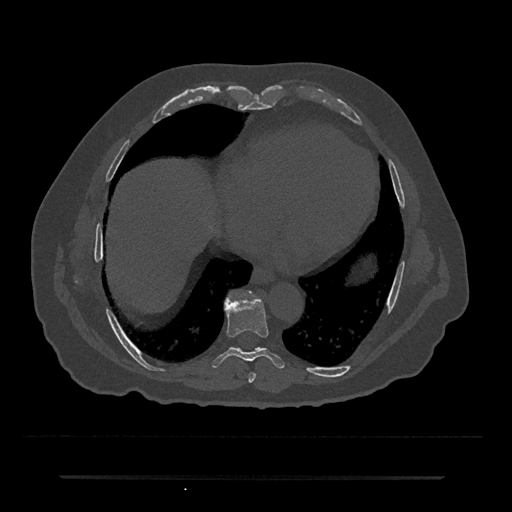
CT including the spine, one axial slice; position 327 of 797 along the scan axis; reconstruction kernel Br40s/3; bone window (W 1800 / L 400 HU); 512 × 512 image matrix. Patient: male, 69 years. Case-level facts recorded for this patient, not image findings: primary cancer: prostate.
Outlined on this slice (semi-automatically segmented with operator editing):
- T7 vertebra: box from (x=248, y=373) to (x=256, y=383) px
- T8 vertebra: (x=212, y=298)–(x=285, y=369)